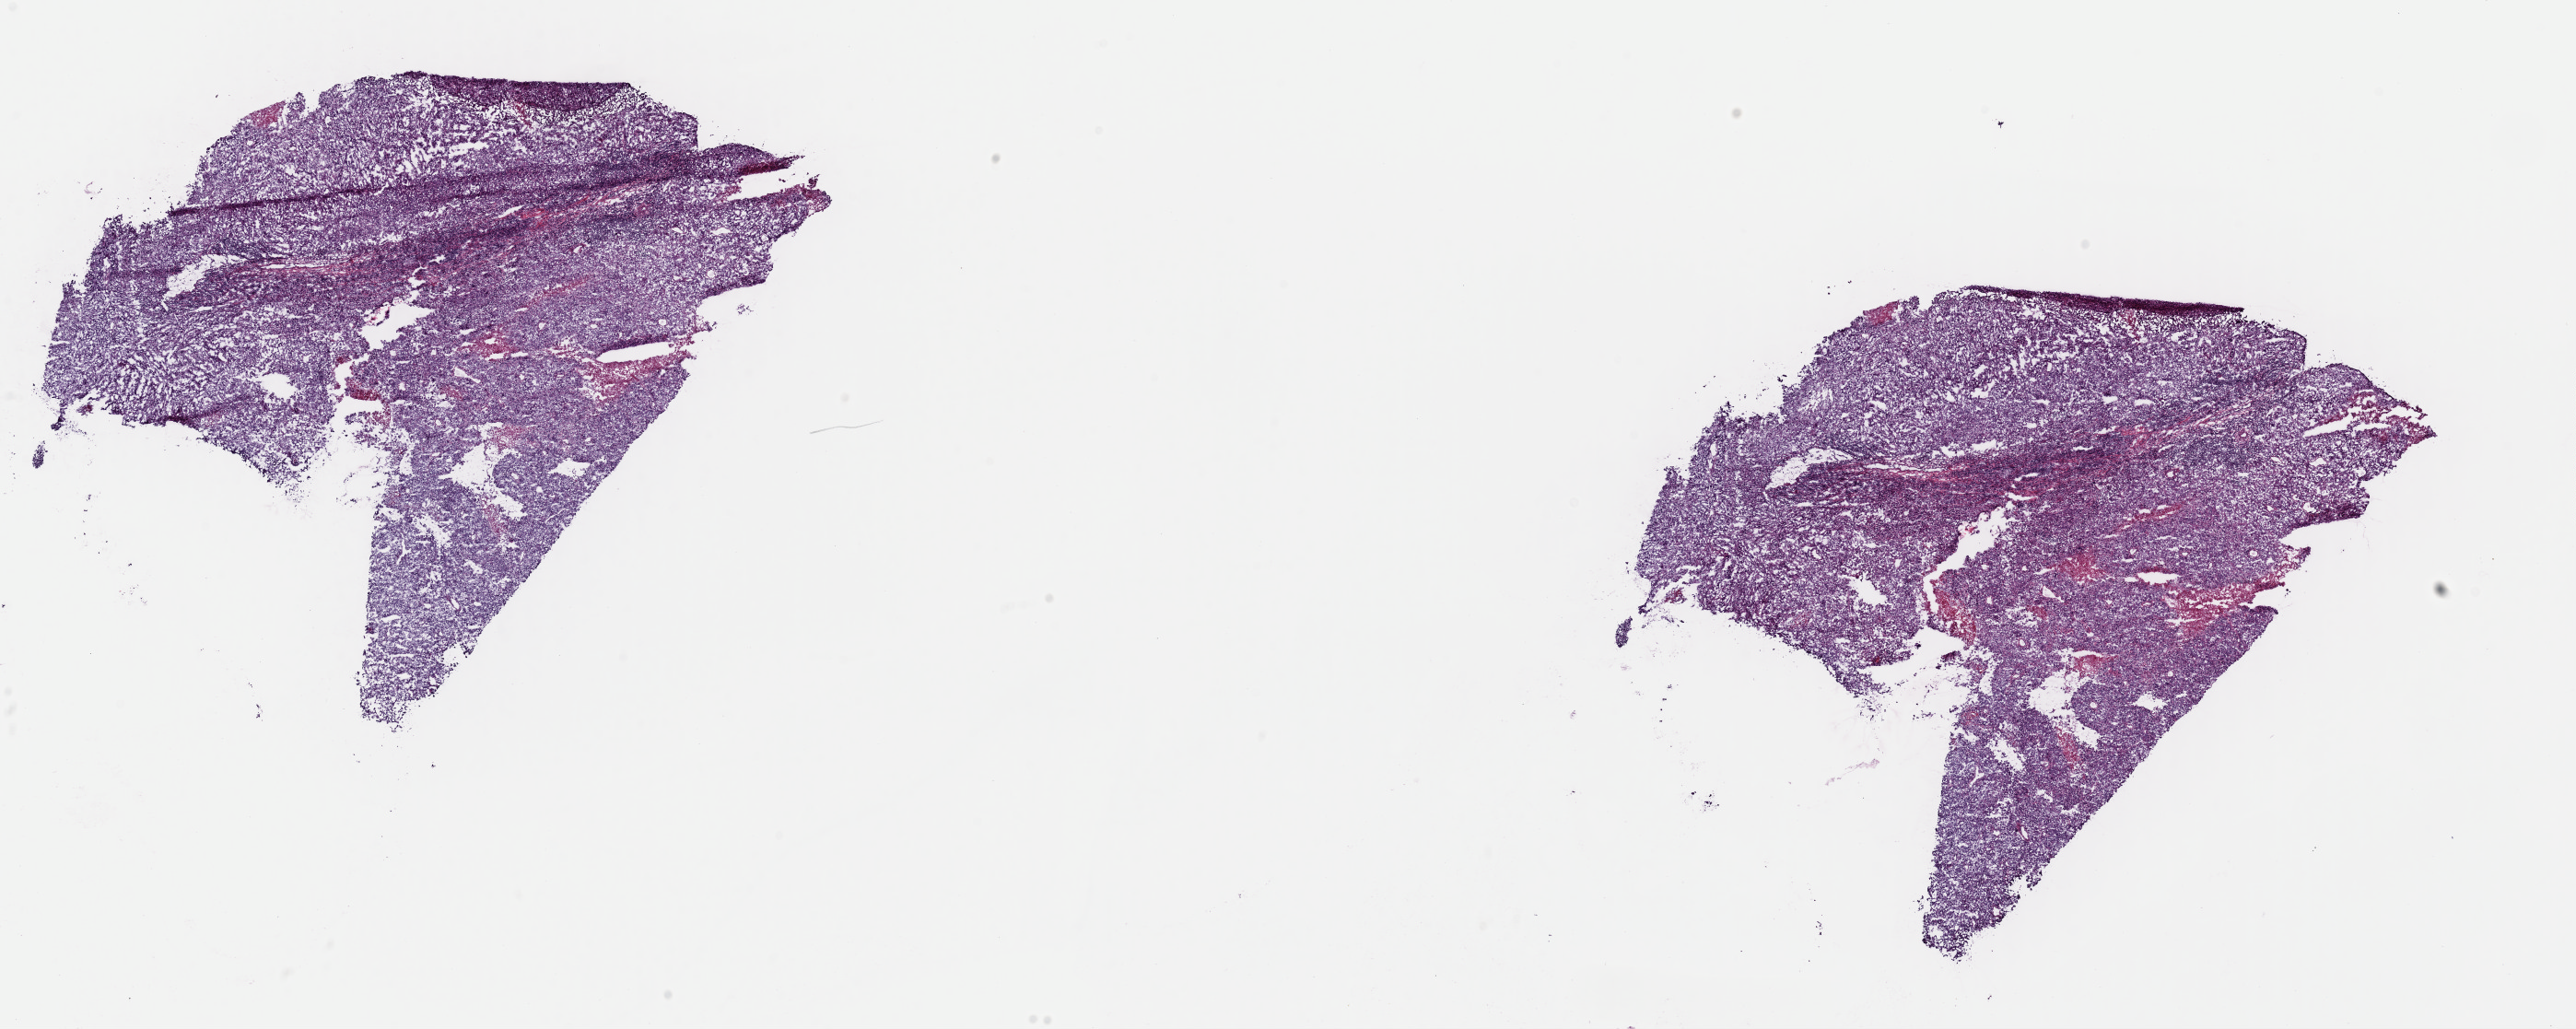
H&E-stained whole-slide image, shown as a low-resolution overview of the whole scanned area (about 22.1 x 8.8 mm, from a 40x scan). Frozen section from the top of the tissue portion. Metastatic tumour sample, sampled site: lymph nodes of axilla or arm. Female, age 33 years at initial diagnosis. Composition of this section per pathologist review: tumour cells 80%, tumour nuclei 90%, normal cells 0%, stromal cells 10%, necrosis 10%. Inflammatory infiltration, as recorded: lymphocyte infiltration 3%, monocyte infiltration 0%, neutrophil infiltration 0%.
This section: metastatic tumour tissue. Patient diagnosis: Malignant melanoma, NOS.